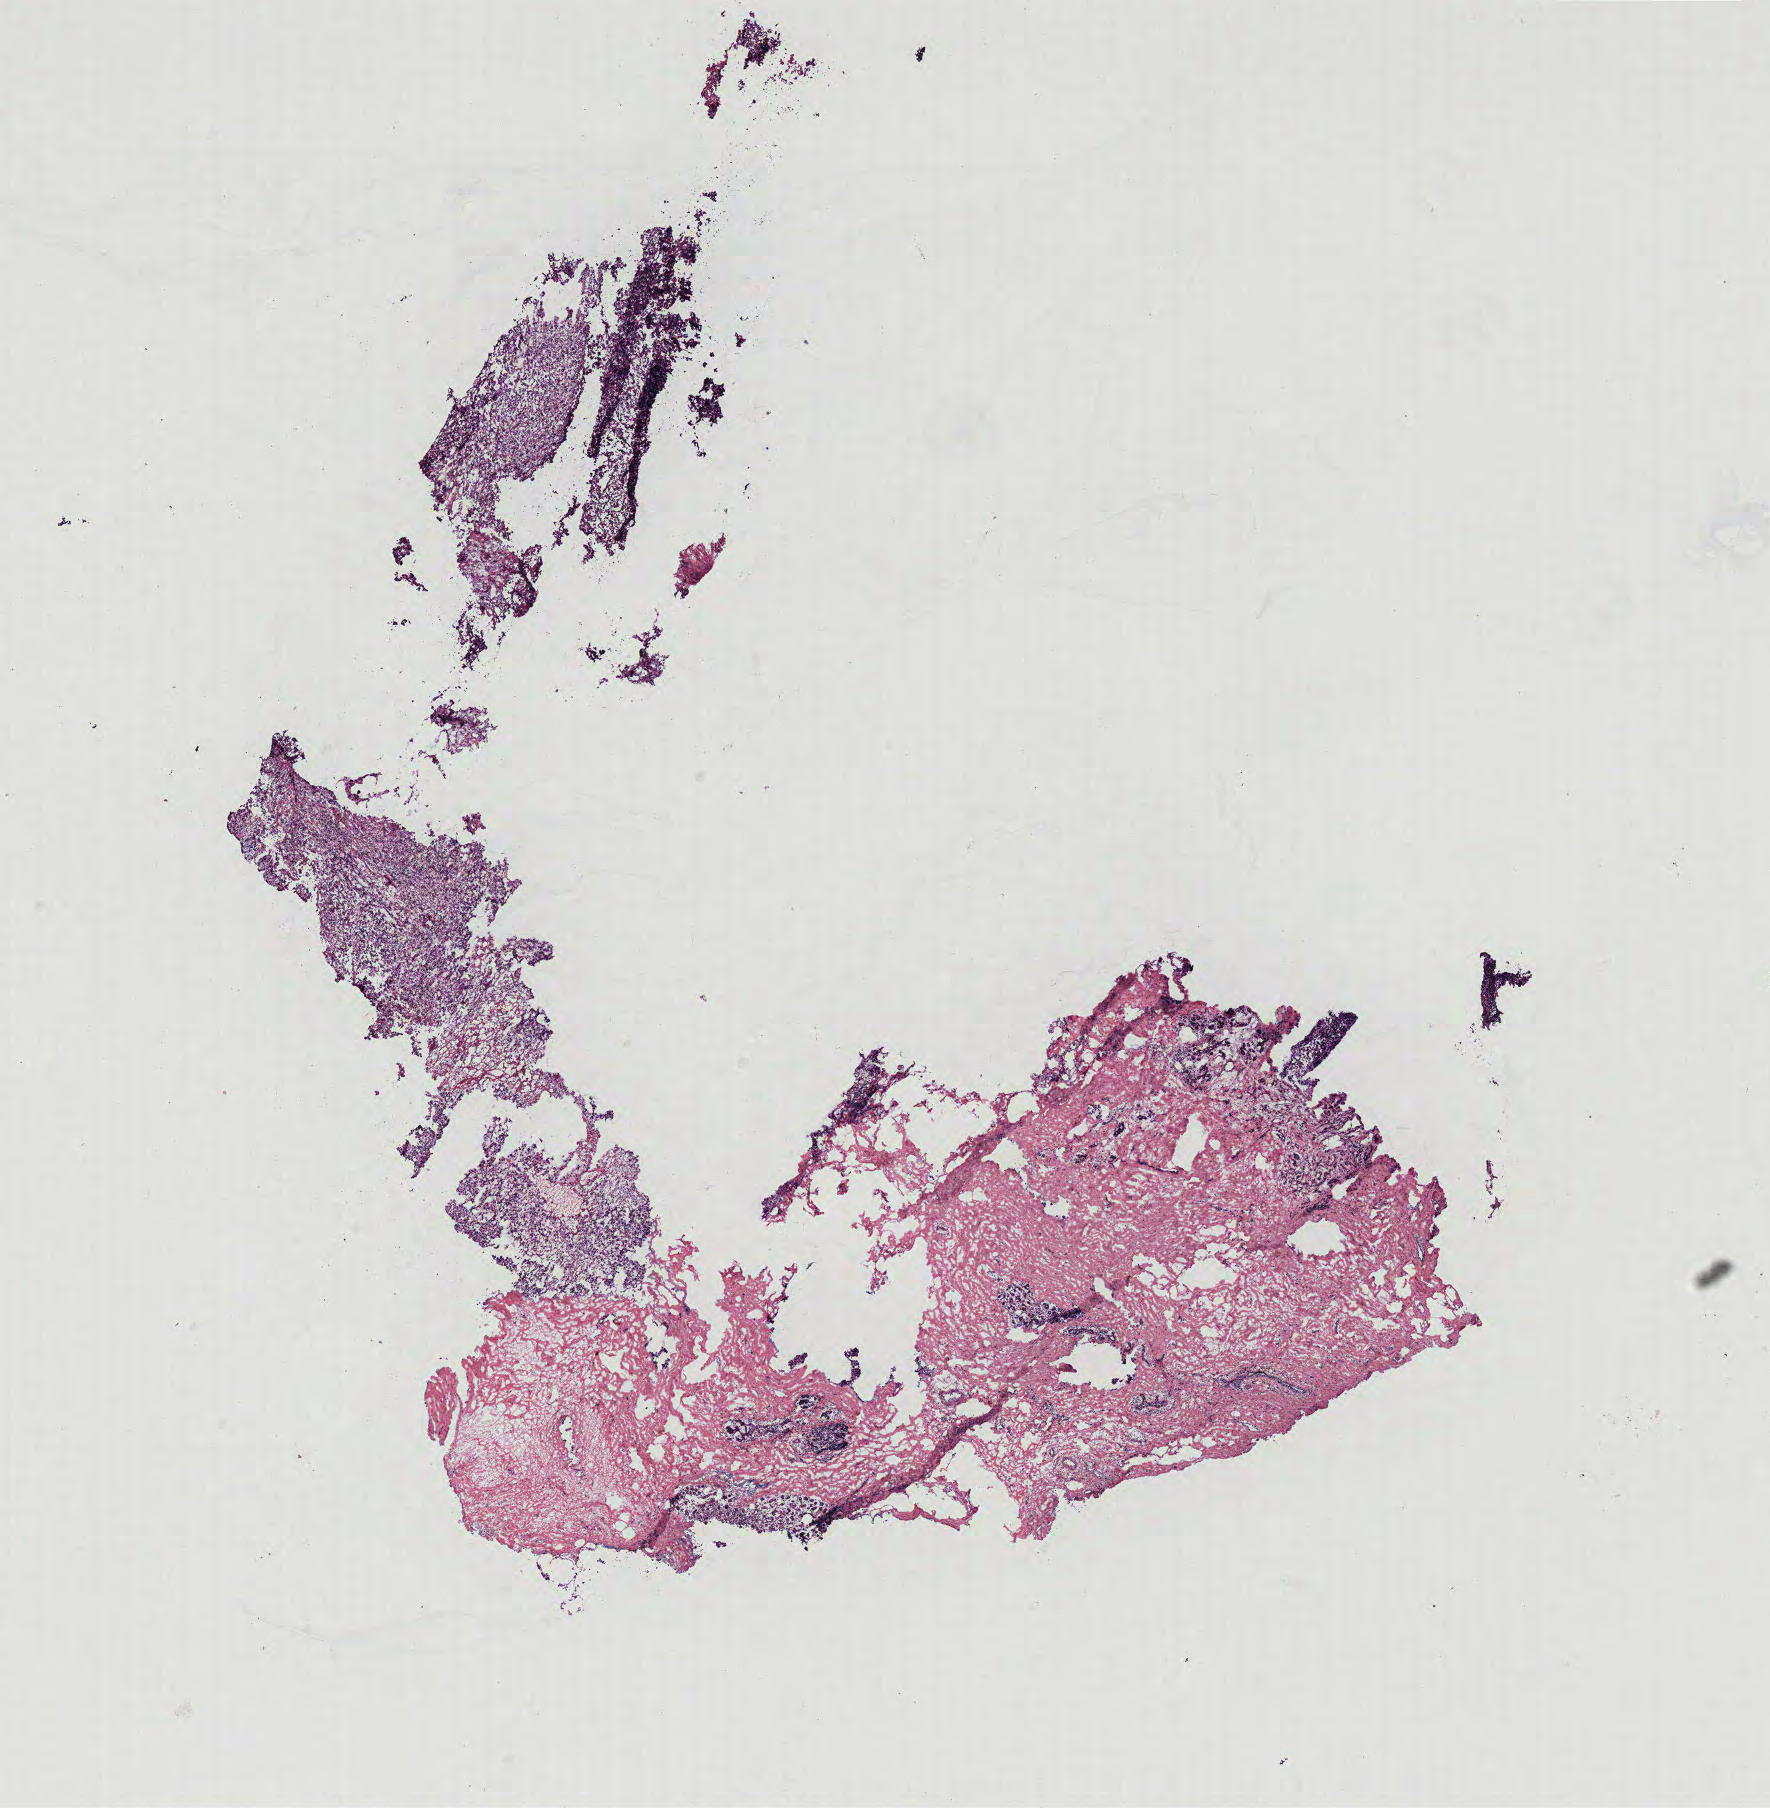
Digitized H&E-stained tissue section (whole slide) — shown as a low-resolution overview of the whole scanned area (about 14.2 x 14.5 mm), breast, tissue type not recorded.
* patient diagnosis (cohort enrolment): breast cancer (breast)